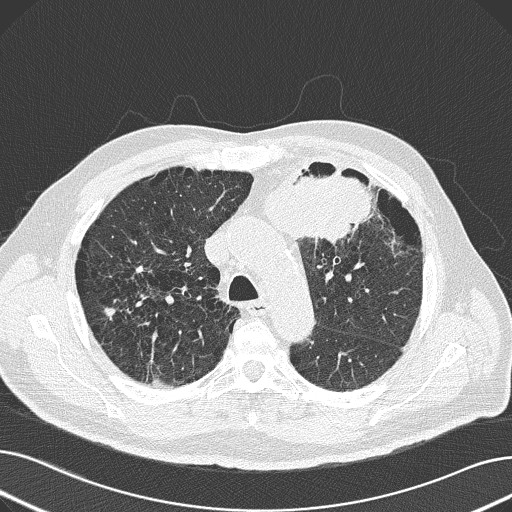
Chest CT (low-dose screening protocol), one axial image. First (baseline) screen. Lung window (W 1500 / L -600 HU). Slice 57 of 165 in the series. Male participant, aged 69 years at enrolment.
Expert-annotated lung lesion, box from (x=227, y=147) to (x=380, y=254) px. Reader record for this screening exam (exam-level; its link to the box is not recorded): non-calcified nodule or mass ≥4 mm, left upper lobe, 6 × 10 mm, spiculated (stellate) margins, soft tissue attenuation. Lung cancer was diagnosed 20 days after this screen: non-small cell carcinoma, left upper lobe, poorly differentiated (G3), stage IB (AJCC 6th edition), 100 mm at pathology.